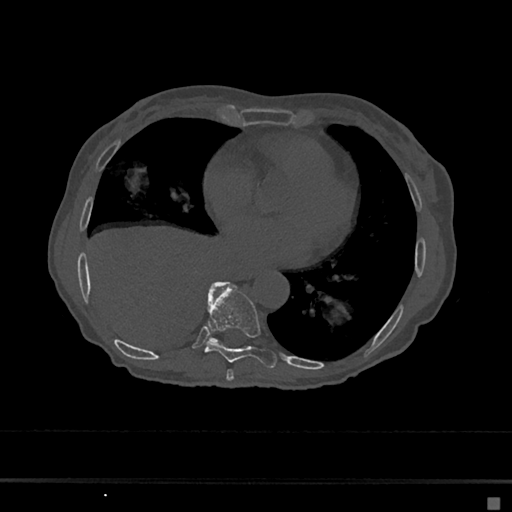
CT including the spine, one axial slice; slice 318 of 797 in the series (ordered by position); reconstruction kernel Br40s/3; bone window (W 1800 / L 400 HU); 0.5 mm slice thickness; 512 × 512 image matrix, field of view 360 × 360 mm. Female patient, age 68 years. From the clinical record (not read from this slice): primary cancer: renal.
Structures marked on this image (semi-automatic segmentation, software-assisted and operator-edited):
- T7 vertebra: bounding box (x1, y1, x2, y2) in pixels: (226, 369, 234, 381)
- T8 vertebra: (204, 282, 277, 369)
- T9 vertebra: (210, 281, 225, 342)